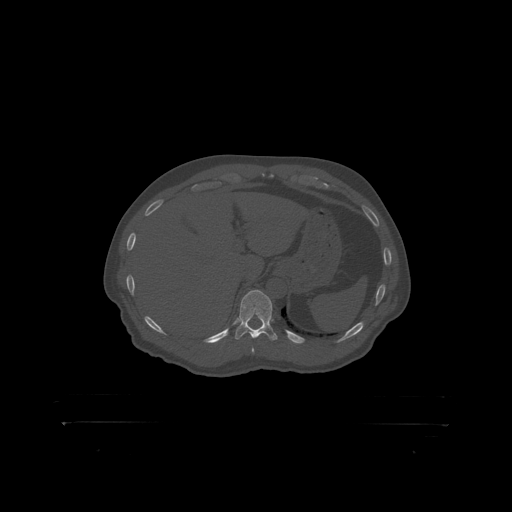
CT including the spine, one axial slice. Position 380 of 399 along the scan axis. 120 kVp. Bone window (W 1800 / L 400 HU). 512 × 512 image matrix, field of view 650 × 650 mm. Patient: male, 46 years. Case-level facts recorded for this patient, not image findings: primary cancer: skin.
Structures marked on this image (semi-automatically segmented with operator editing):
- T11 vertebra: bounding box (x1, y1, x2, y2) in pixels: (239, 290, 273, 319)